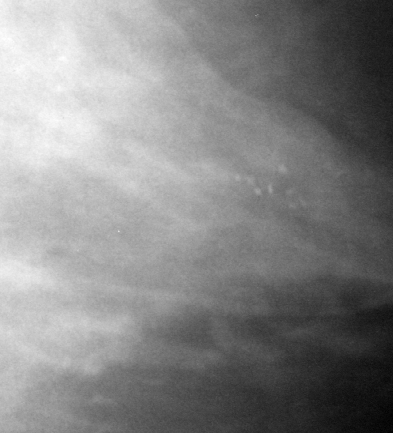
Crop from a digitized film mammogram around one marked abnormality, left breast, MLO view, BI-RADS breast density category 3 (scale 1–4).
- Finding: calcifications, morphology punctate, distribution clustered; BI-RADS assessment category 4; subtlety rating 3 on a 1 (subtle) to 5 (obvious) scale; pathology (as recorded): benign.